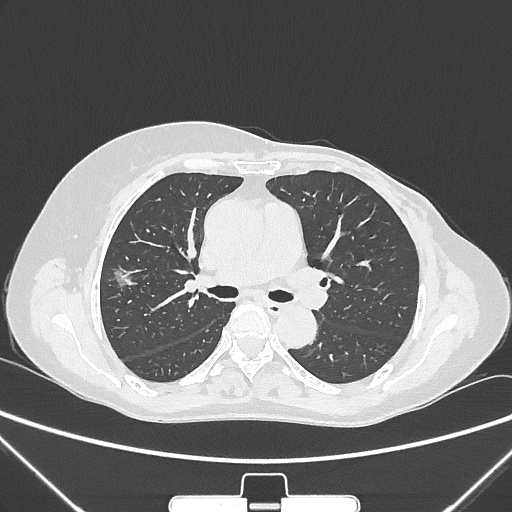
Chest CT, one axial slice. Slice 155 of 265 in the series (ordered by position). Lung window (W 1500 / L -600 HU). 512 × 512 image matrix. Female patient, age 64 years. From the clinical record (not read from this slice): clinical TNM (as recorded): T1c N0 M0; histopathological grade: G1-2.
Outlined on this slice (rectangle marked by the reading radiologist):
- lung tumour (recorded histology: adenocarcinoma): bounding box (x1, y1, x2, y2) in pixels: (113, 258, 140, 297)